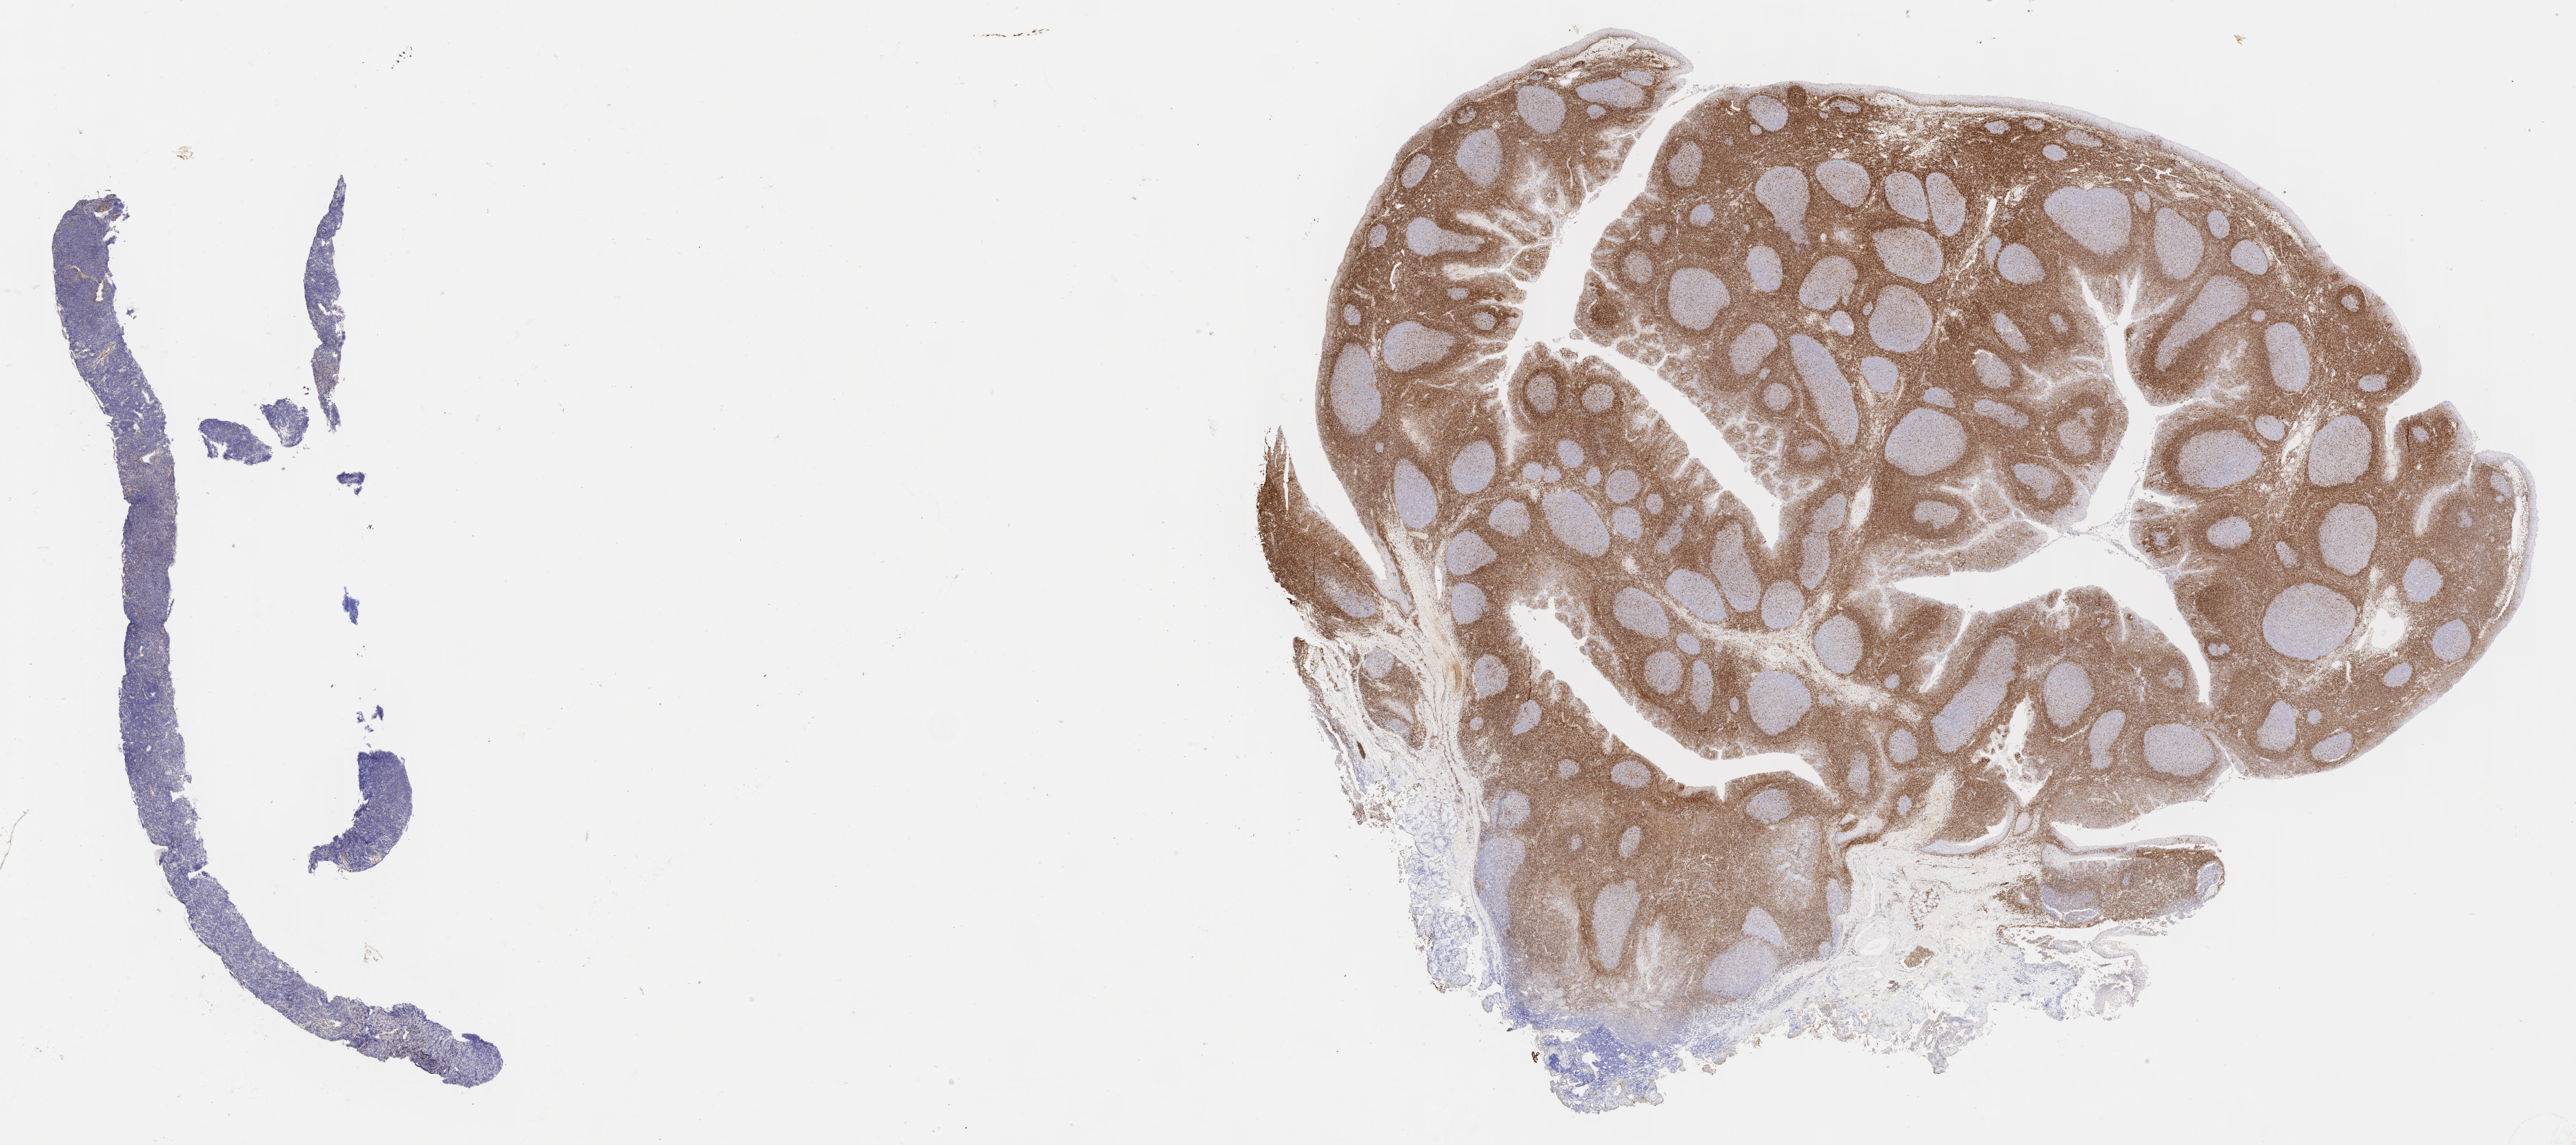
Whole-slide image, immunohistochemical stain for BCL2 — shown as a low-resolution overview of the whole scanned area (about 30.2 x 13.4 mm), specimen: tumor tissue, anatomic site: ovary. Female patient; age at initial diagnosis 9 years.
• histologic diagnosis: Burkitt lymphoma, NOS